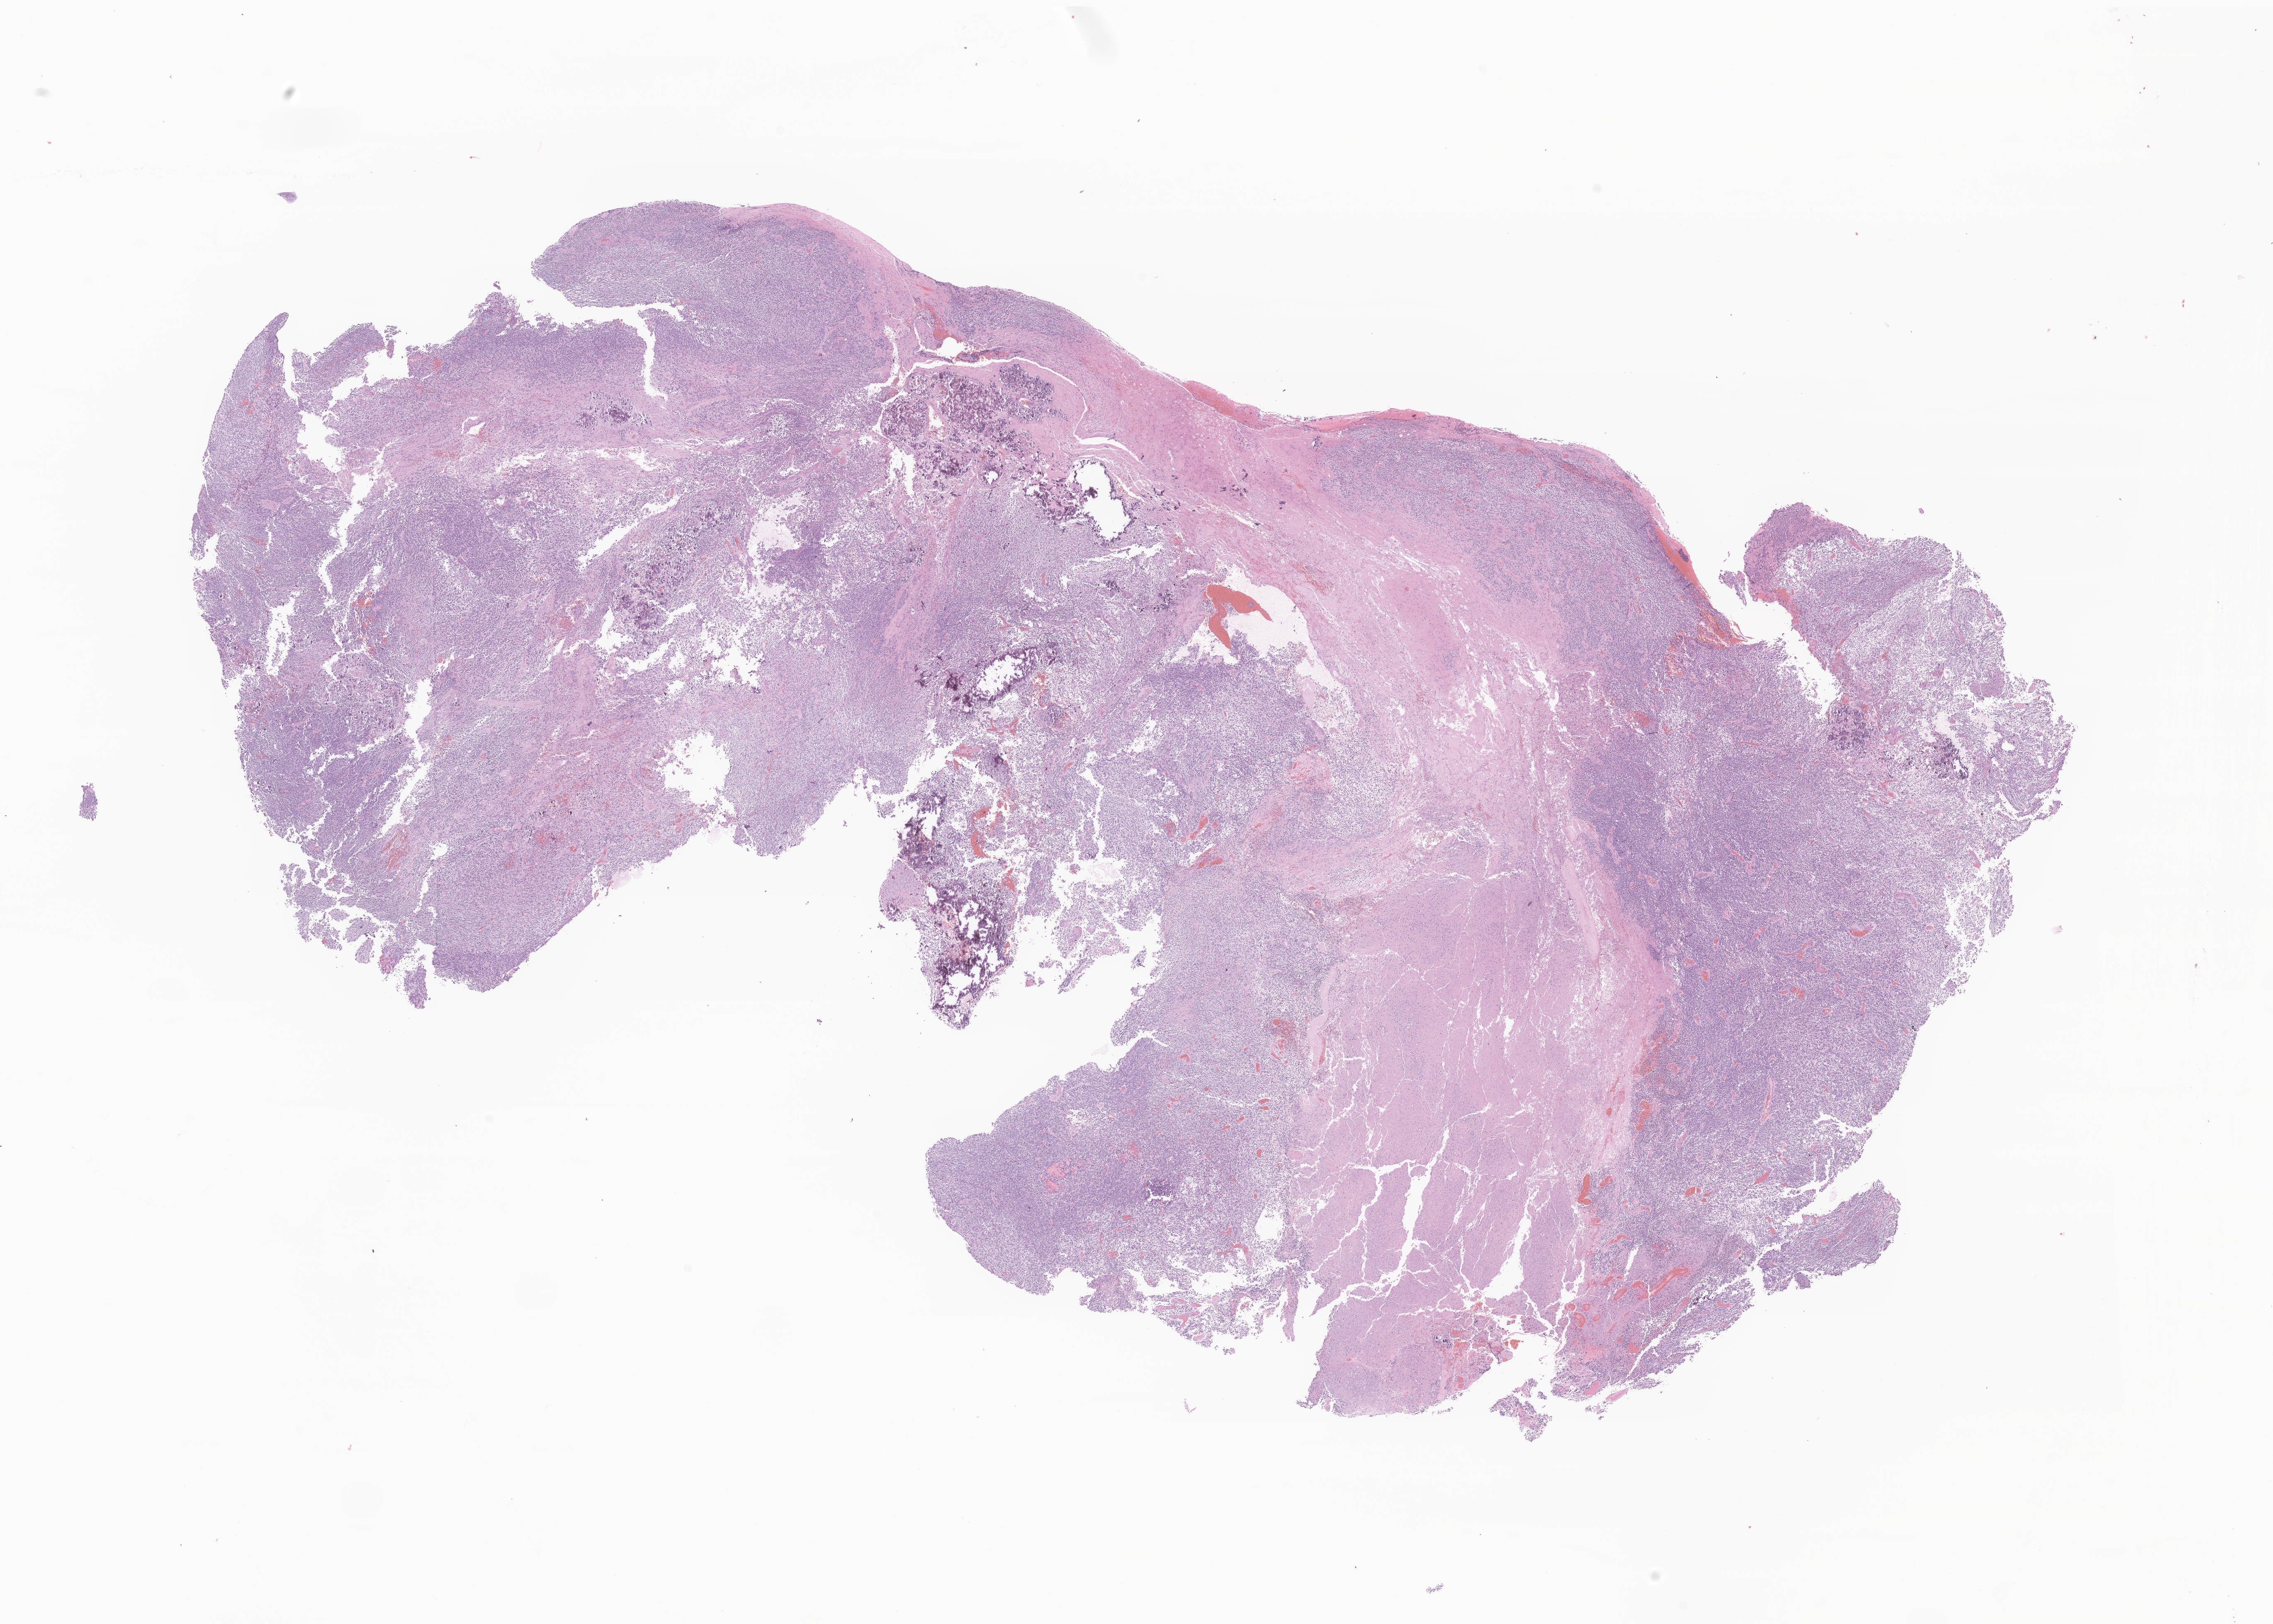
Digitized hematoxylin and eosin (H&E)-stained section of tumor tissue from the brain, low-resolution overview of the scanned area, about 23.1 x 16.5 mm, FFPE section. Patient male; age 148 months (12 years 4 months).
Recorded diagnosis: Medulloblastoma, NOS.